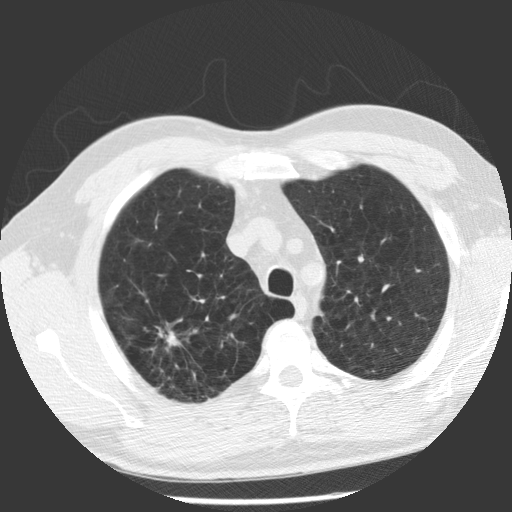
Low-dose screening chest CT, one axial slice; slice 90 of 112 in the series (ordered by position); lung window (W 1500 / L -600 HU); 2.5 mm slice thickness; 512 × 512 image matrix.
Annotated regions visible in this slice (outlined manually by an expert reader):
- lesion 1 (tumor, upper lobe of right lung): bounding box <166,330,179,347> (left, top, right, bottom; pixels)